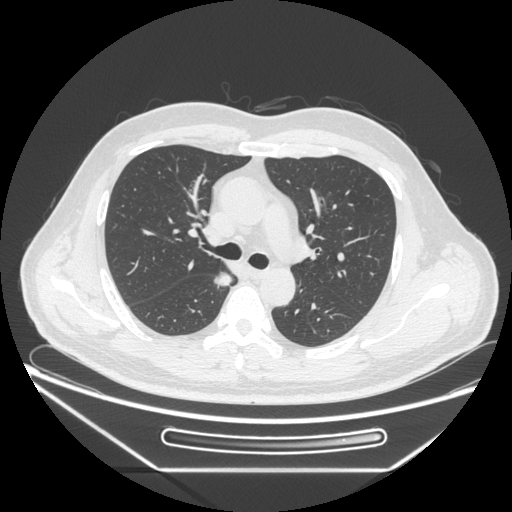
Chest CT, one axial slice. Reconstruction kernel STANDARD. 120 kVp. Lung window (W 1500 / L -600 HU). 1.25 mm slice thickness. 512 × 512 image matrix, field of view 414 × 414 mm. Patient: male, 49 years. Case-level facts recorded for this patient, not image findings: clinical TNM (as recorded): T1b N0 M0; histopathological grade: G2.
Outlined on this slice (rectangle marked by the reading radiologist):
- lung tumour (recorded histology: adenocarcinoma): box from (x=210, y=268) to (x=236, y=294) px